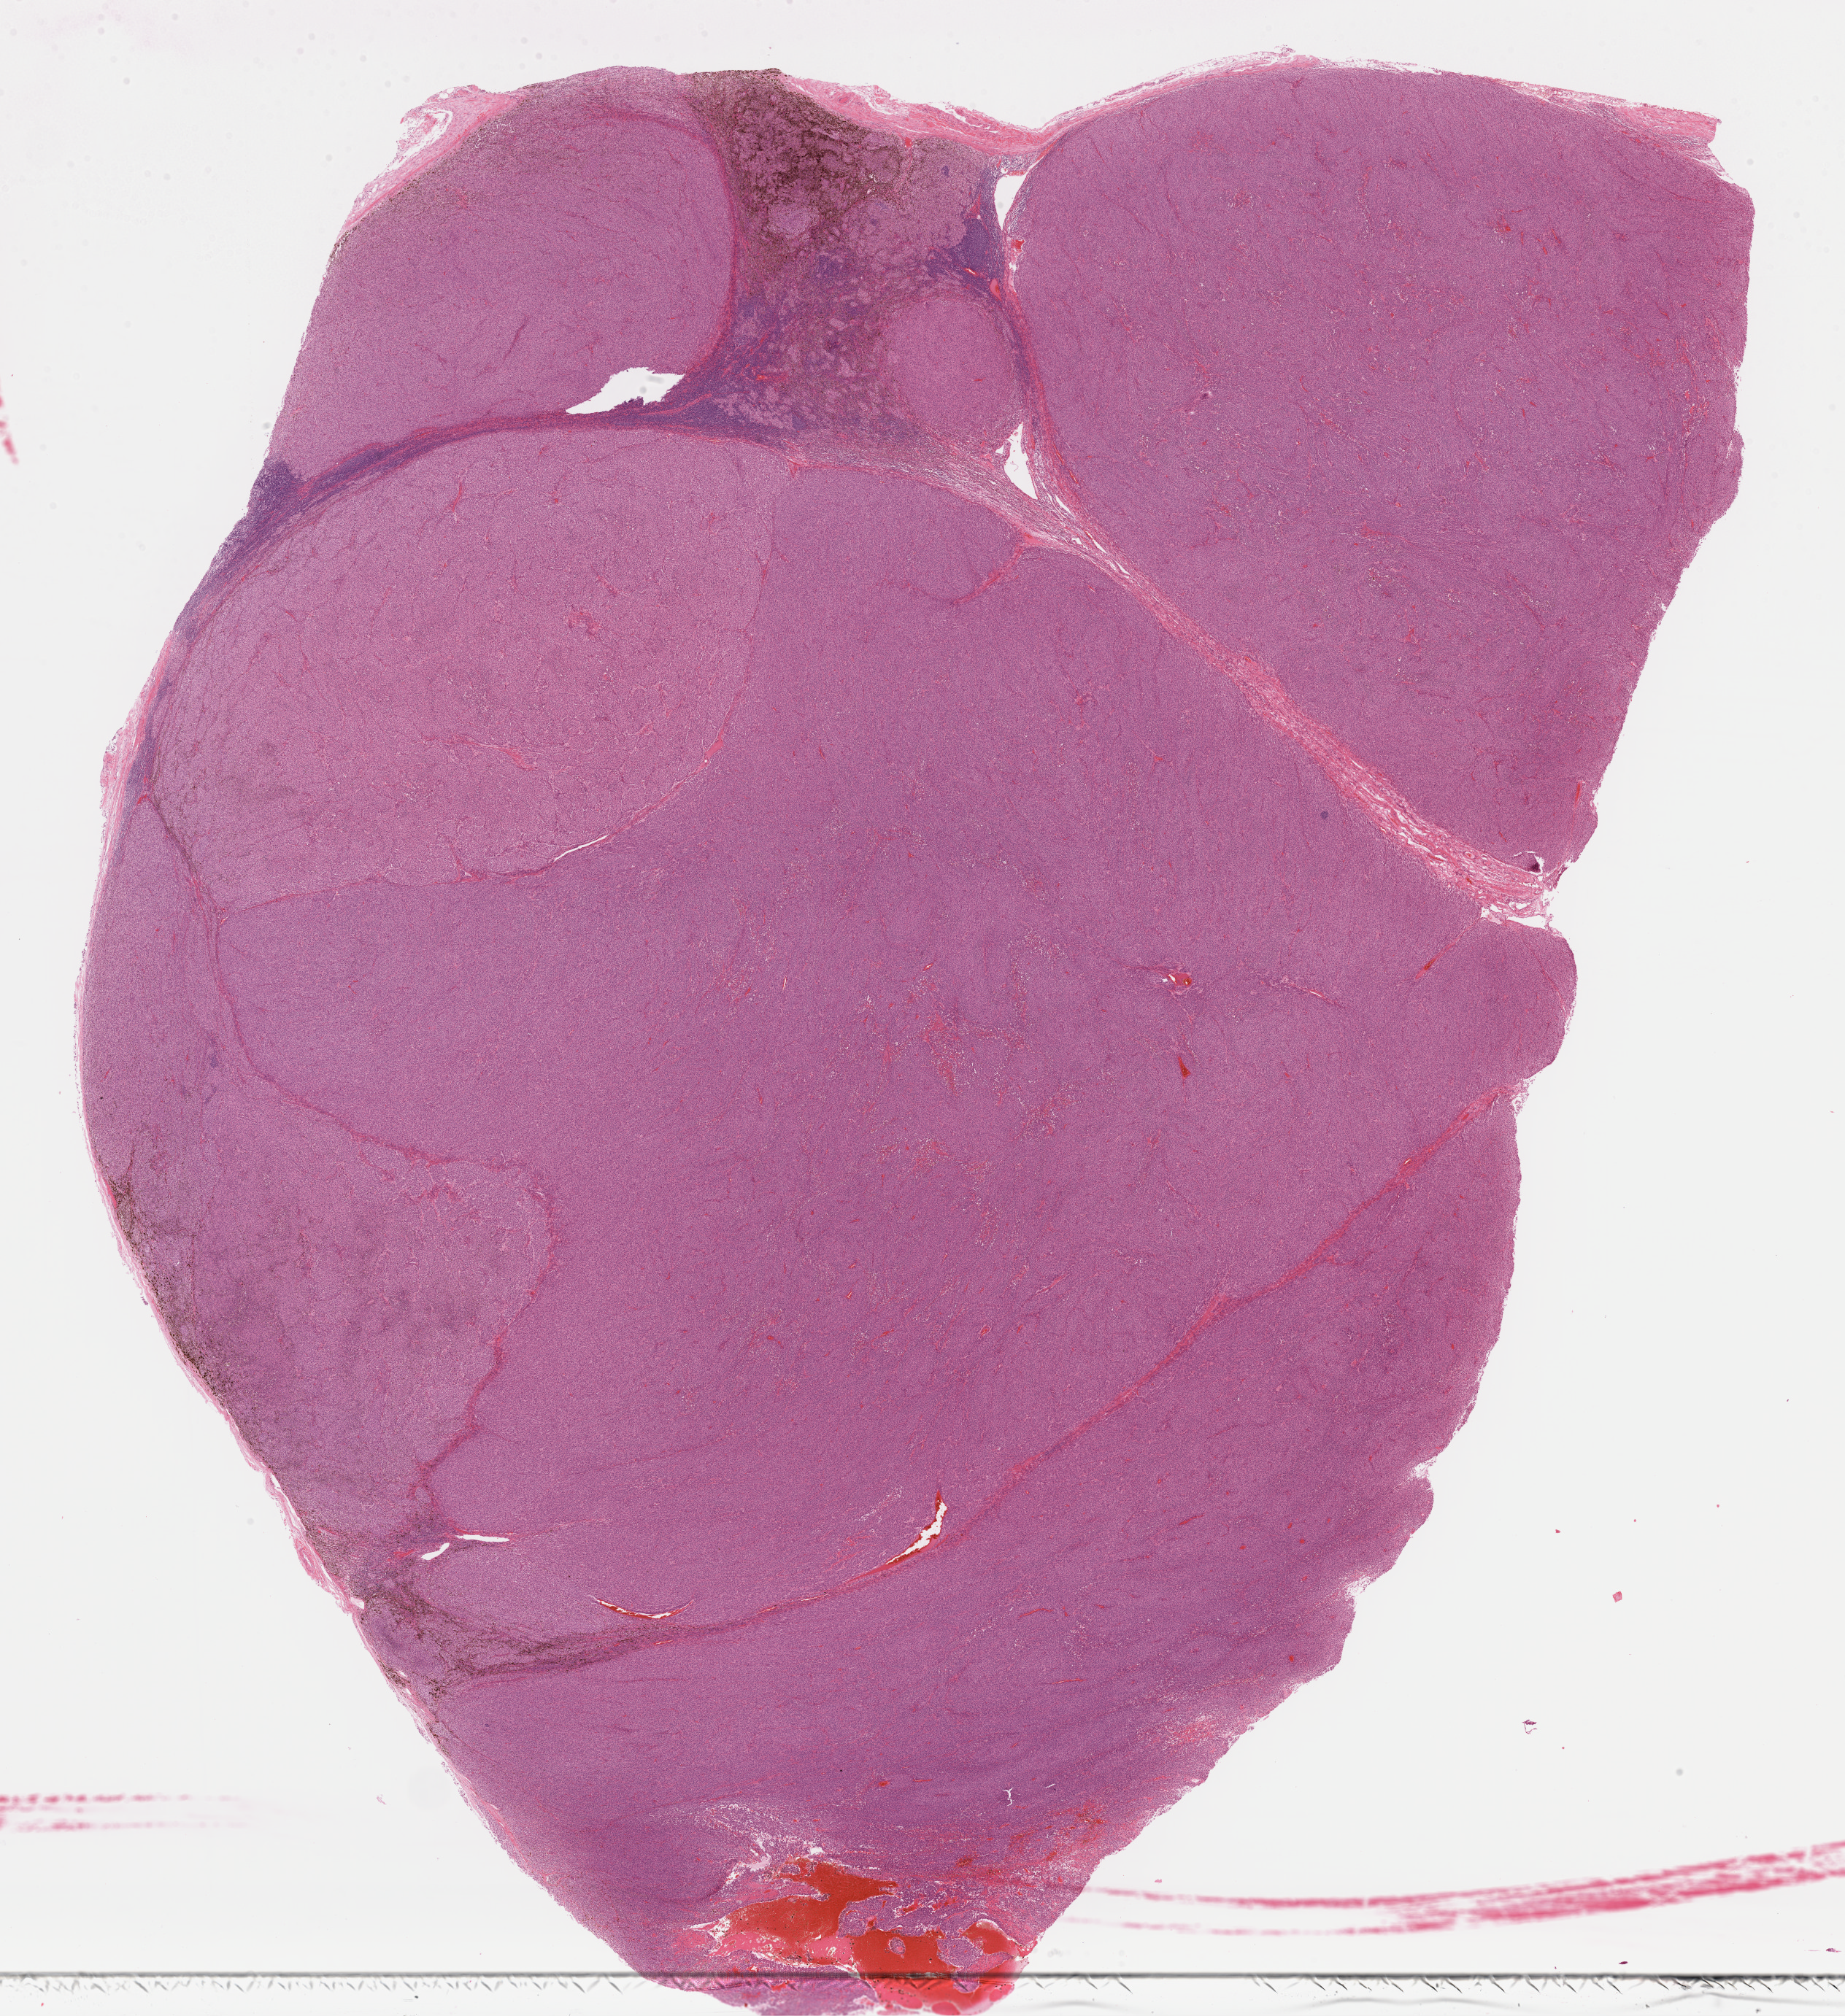
Whole-slide histology image, H&E-stained, shown as a low-resolution overview of the whole scanned area (about 20.0 x 21.8 mm, acquisition: 40x scan), formalin-fixed paraffin-embedded (FFPE) diagnostic section, metastatic tumour sample, sampled site: lymph nodes of inguinal region or leg. Male, age 55 years at initial diagnosis.
This section: metastatic tumour tissue. Patient diagnosis: Malignant melanoma, NOS.